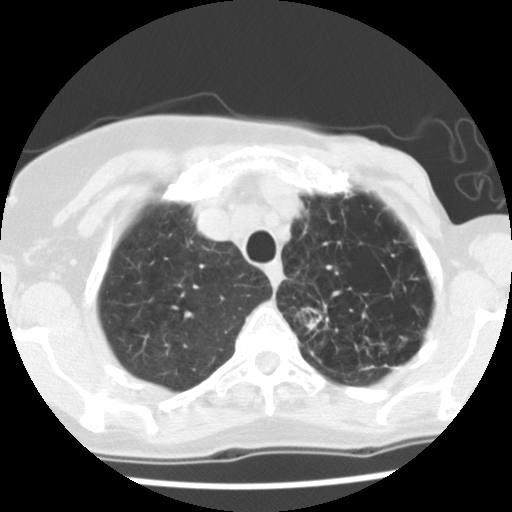
Low-dose screening chest CT, one axial slice. Position 106 of 128 along the scan axis. 140 kVp. Lung window (W 1500 / L -600 HU). 2.5 mm slice thickness. 512 × 512 image matrix, field of view 290 × 290 mm.
Structures marked on this image (expert manual segmentation):
- lesion 1 (tumor, upper lobe of left lung): box from (x=298, y=307) to (x=322, y=330) px